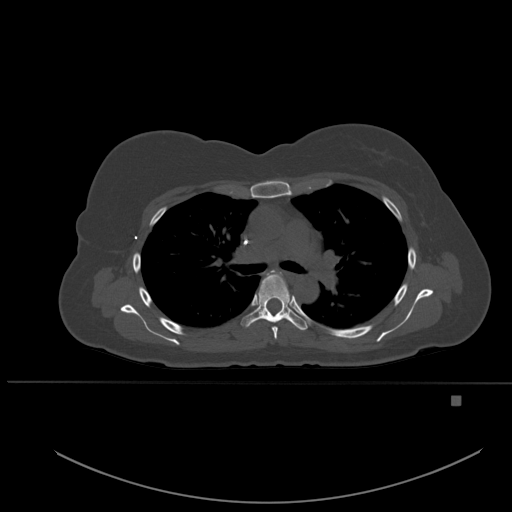
CT including the spine, one axial slice. Slice 369 of 651 in the series (ordered by position). Bone window (W 1800 / L 400 HU). 1.5 mm slice thickness. 512 × 512 image matrix, field of view 443 × 443 mm. Patient: female, 49 years. Case-level facts recorded for this patient, not image findings: primary cancer: breast; vertebrae with lytic lesions (as recorded): L3, T12, L4.
Annotated regions visible in this slice (semi-automatically segmented with operator editing):
- T4 vertebra: bounding box <262,270,282,339> (left, top, right, bottom; pixels)
- T5 vertebra: <241,273,308,330>